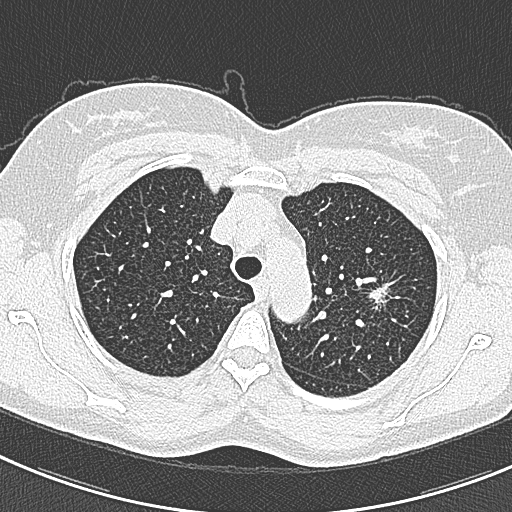
Axial slice from a low-dose chest CT screening exam; baseline annual screen; lung window (W 1500 / L -600 HU); 1 mm slice thickness; lung (sharp) reconstruction kernel (B80f). Female, age 57 years at enrolment.
Expert reader's lesion annotation, box from (x=362, y=271) to (x=412, y=322) px. The screening reader recorded 2 non-calcified nodules or masses ≥4 mm on this exam; which of them this box marks is not recorded. Lung cancer was diagnosed 198 days after this screen: adenocarcinoma, NOS, left upper lobe, well differentiated (G1), stage IA (AJCC 6th edition), 10 mm at pathology.